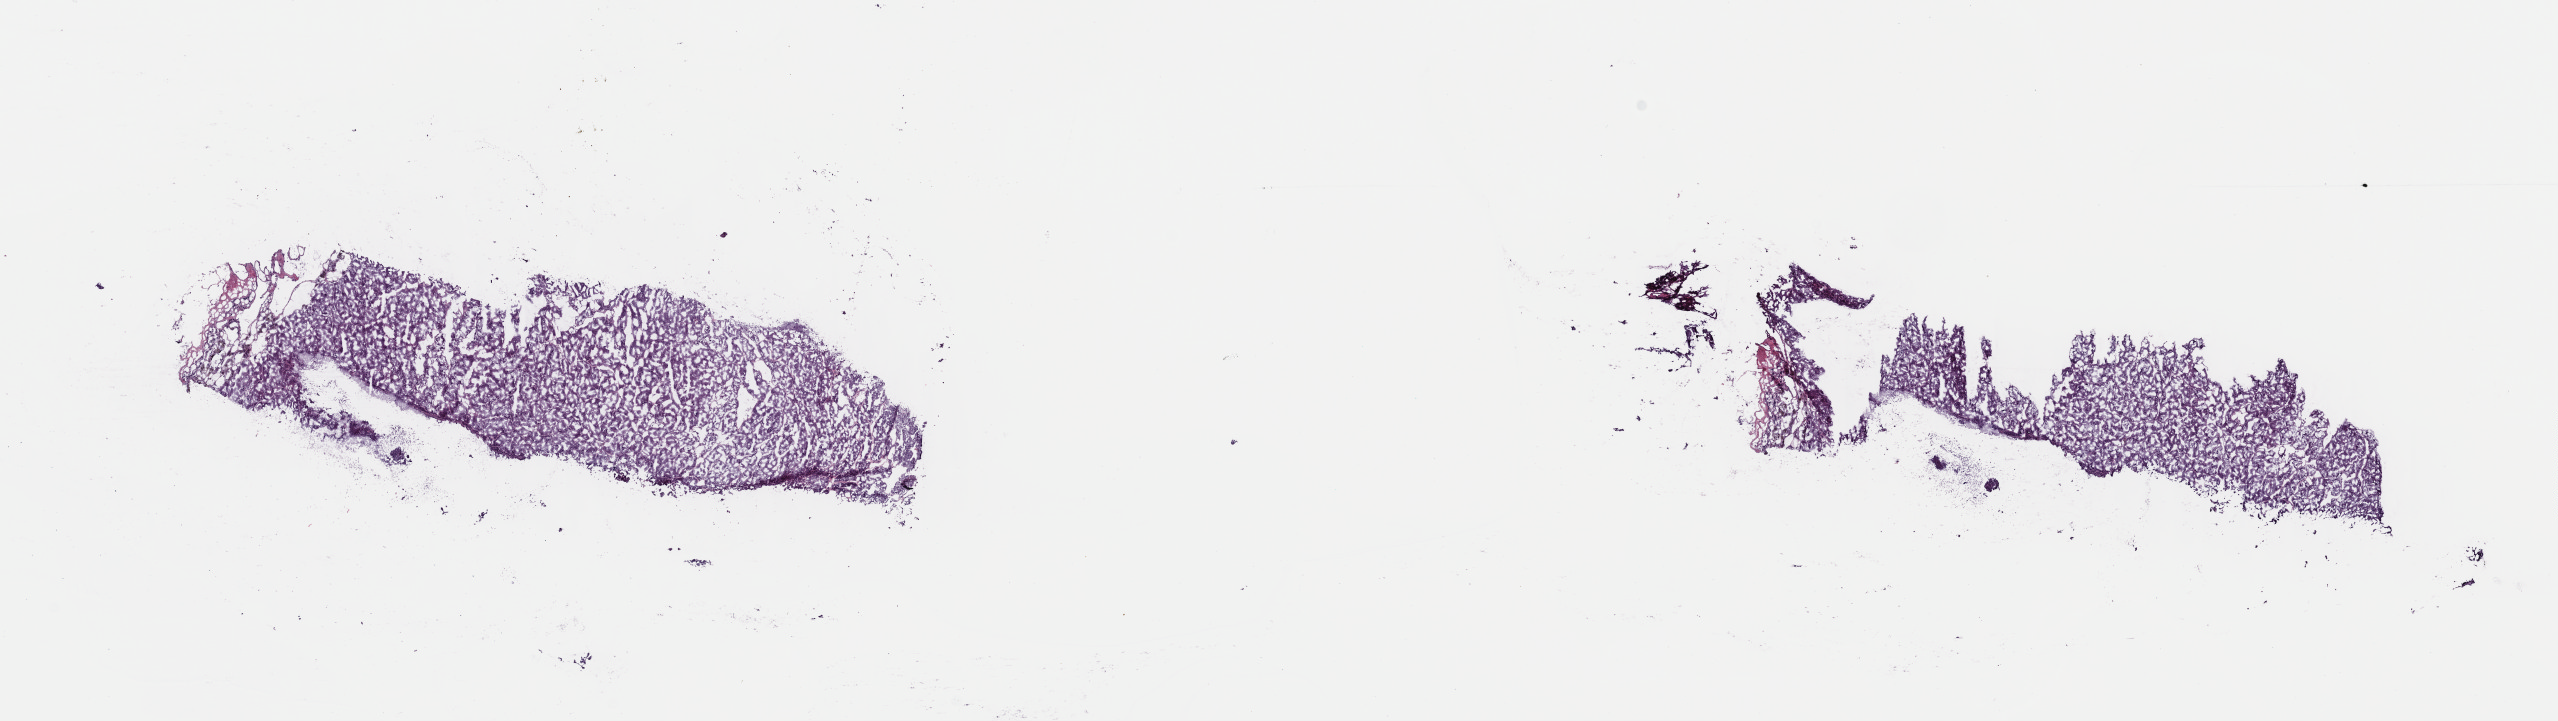
Digitized Hematoxylin and eosin (H&E) stained tissue section (whole slide), whole scanned area (about 20.2 x 5.7 mm, acquisition: 40x scan) shown as a low-resolution overview, frozen section from the top of the tissue portion, sample: primary tumour, adrenal cortex. Female, age 67 years at initial diagnosis. Composition of this section per pathologist review: tumour cells 85%, tumour nuclei 90%, normal cells 0%, stromal cells 15%, necrosis 0%. Inflammatory infiltration, as recorded: lymphocyte infiltration 0%, monocyte infiltration 0%, neutrophil infiltration 0%.
• diagnosis: Adrenal cortical carcinoma (cortex of adrenal gland)